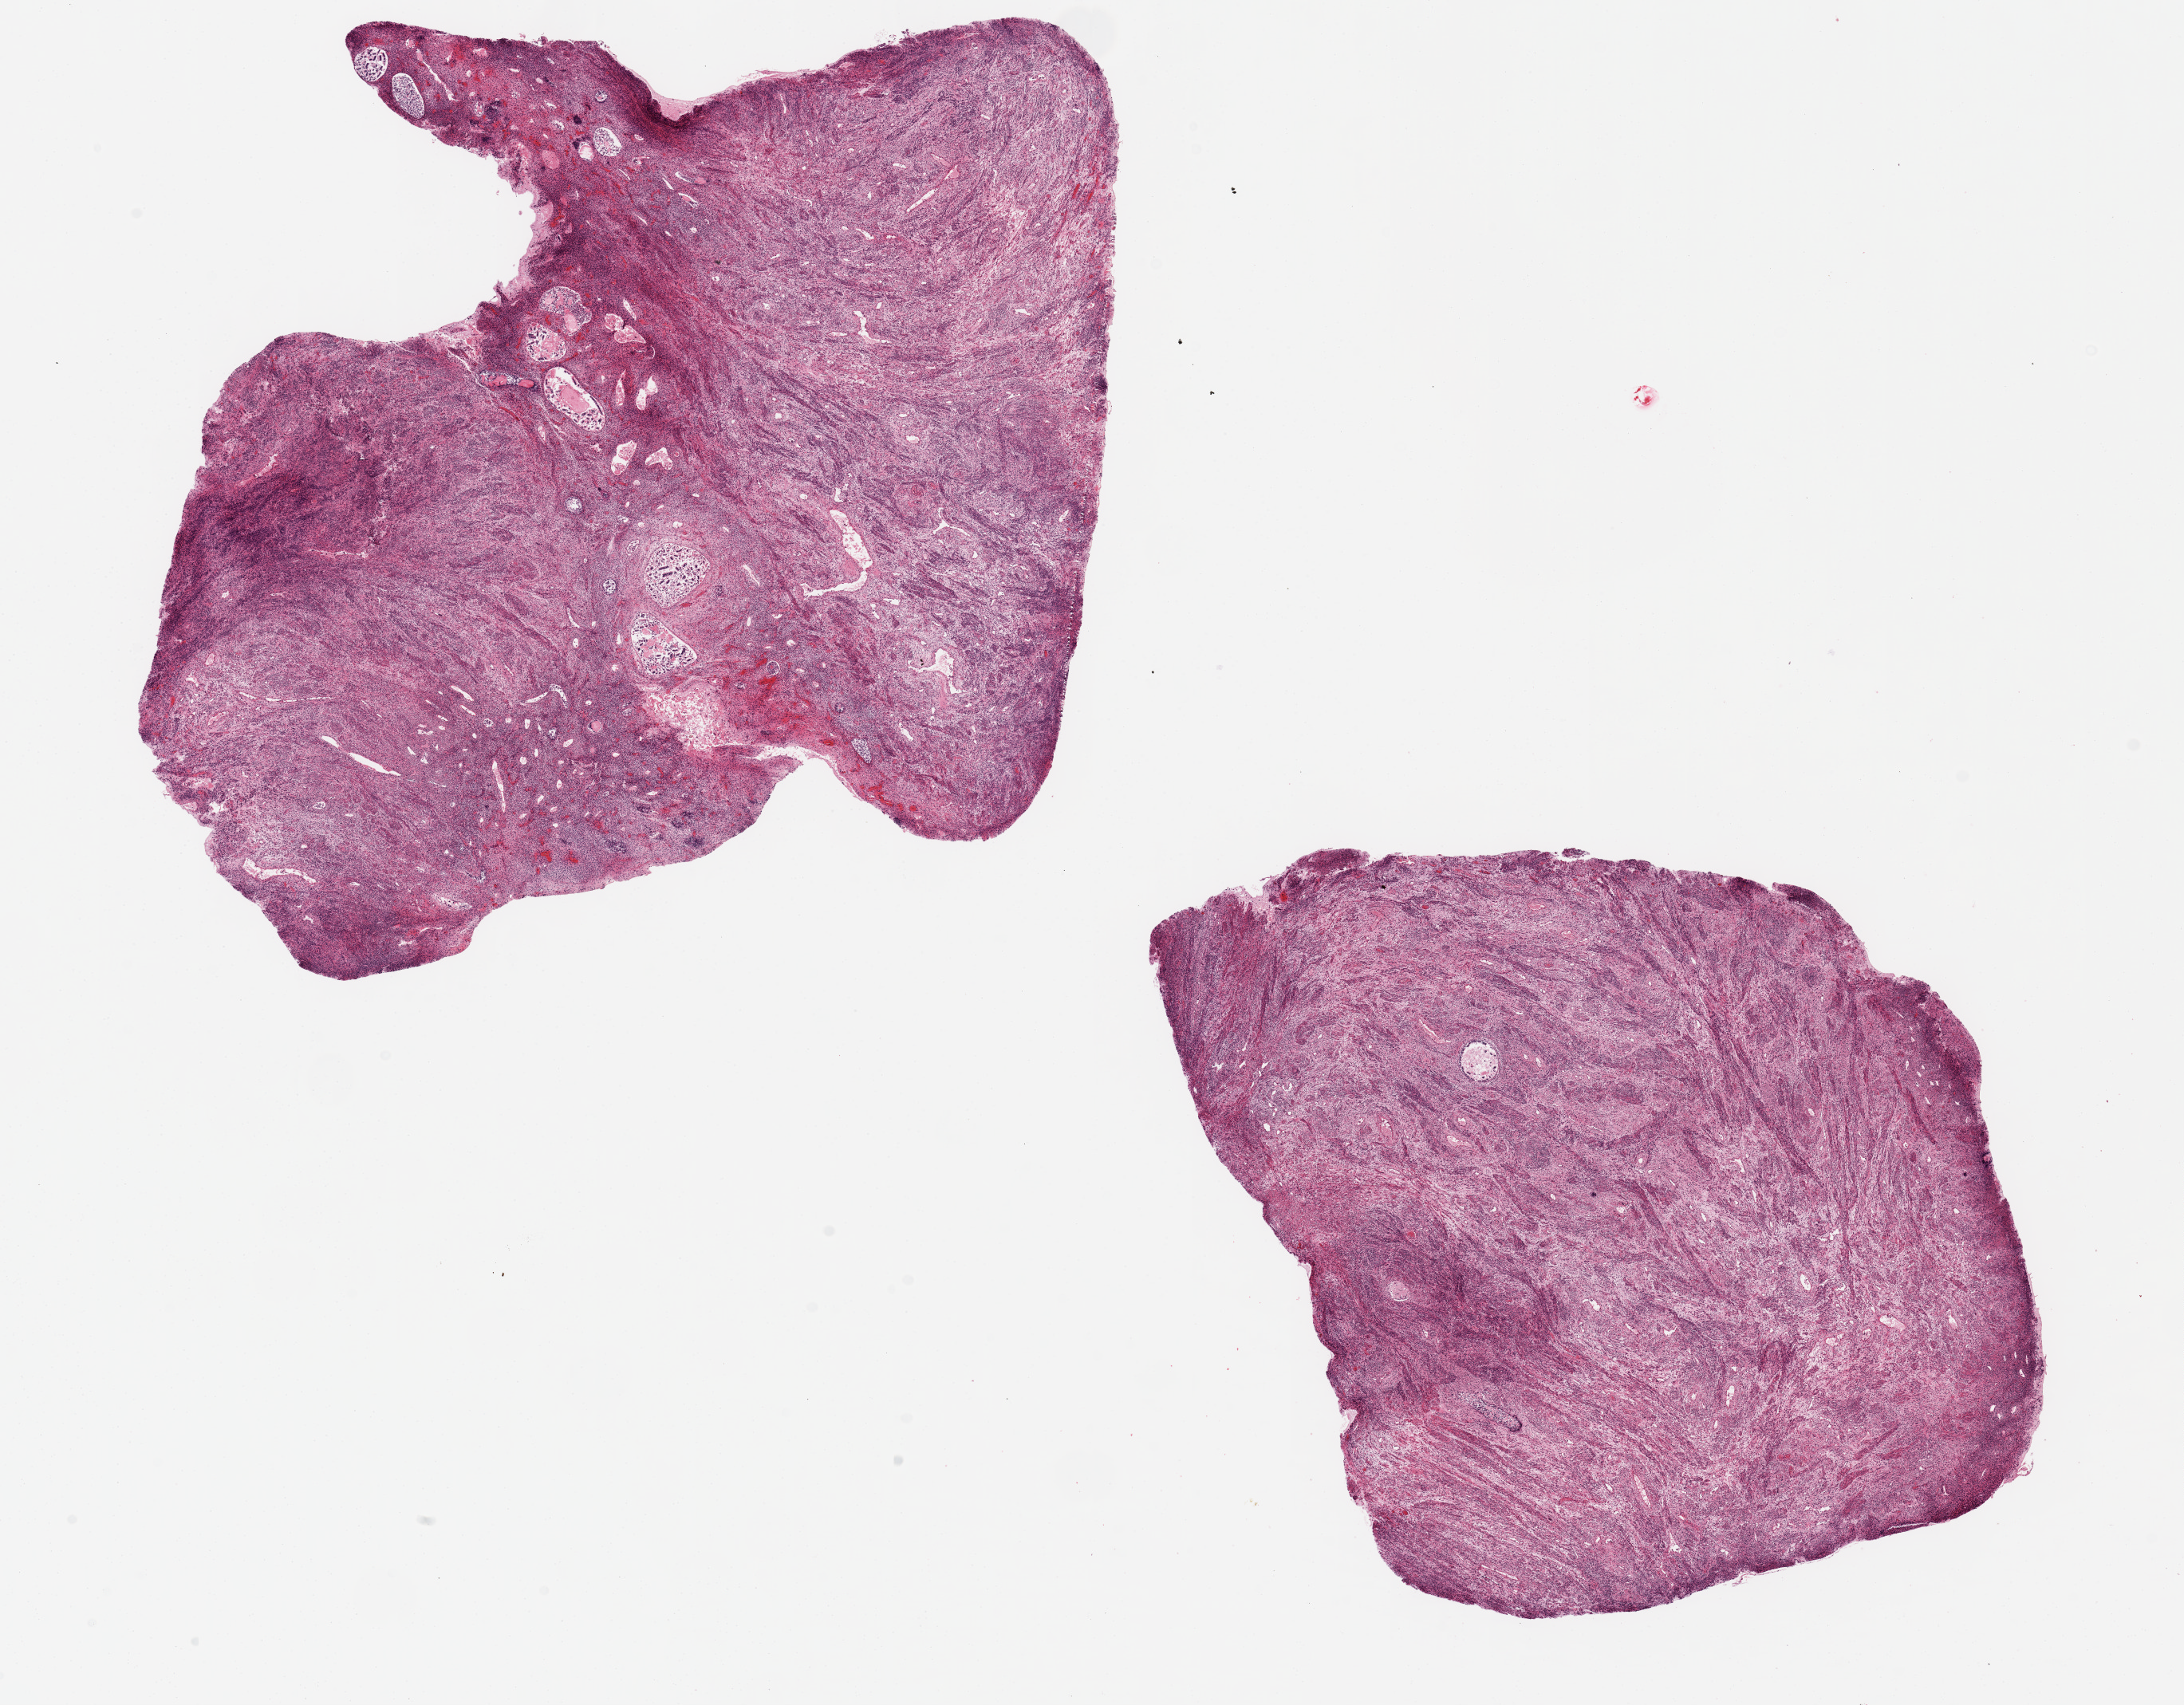
Digitized hematoxylin and eosin (H&E)-stained section — shown as a low-resolution overview of the whole scanned area (about 21.7 x 16.9 mm, acquisition: 20x scan), PAXgene-fixed paraffin-embedded (PFPE) section, section of uterus (target tissue), tissue donor sample.
Pathologist's review note for this sample: 2 ~ 8.5x7mm aliquots, few foci of completely autolyzed mucosa/adenomyosis; mainly myometrium.